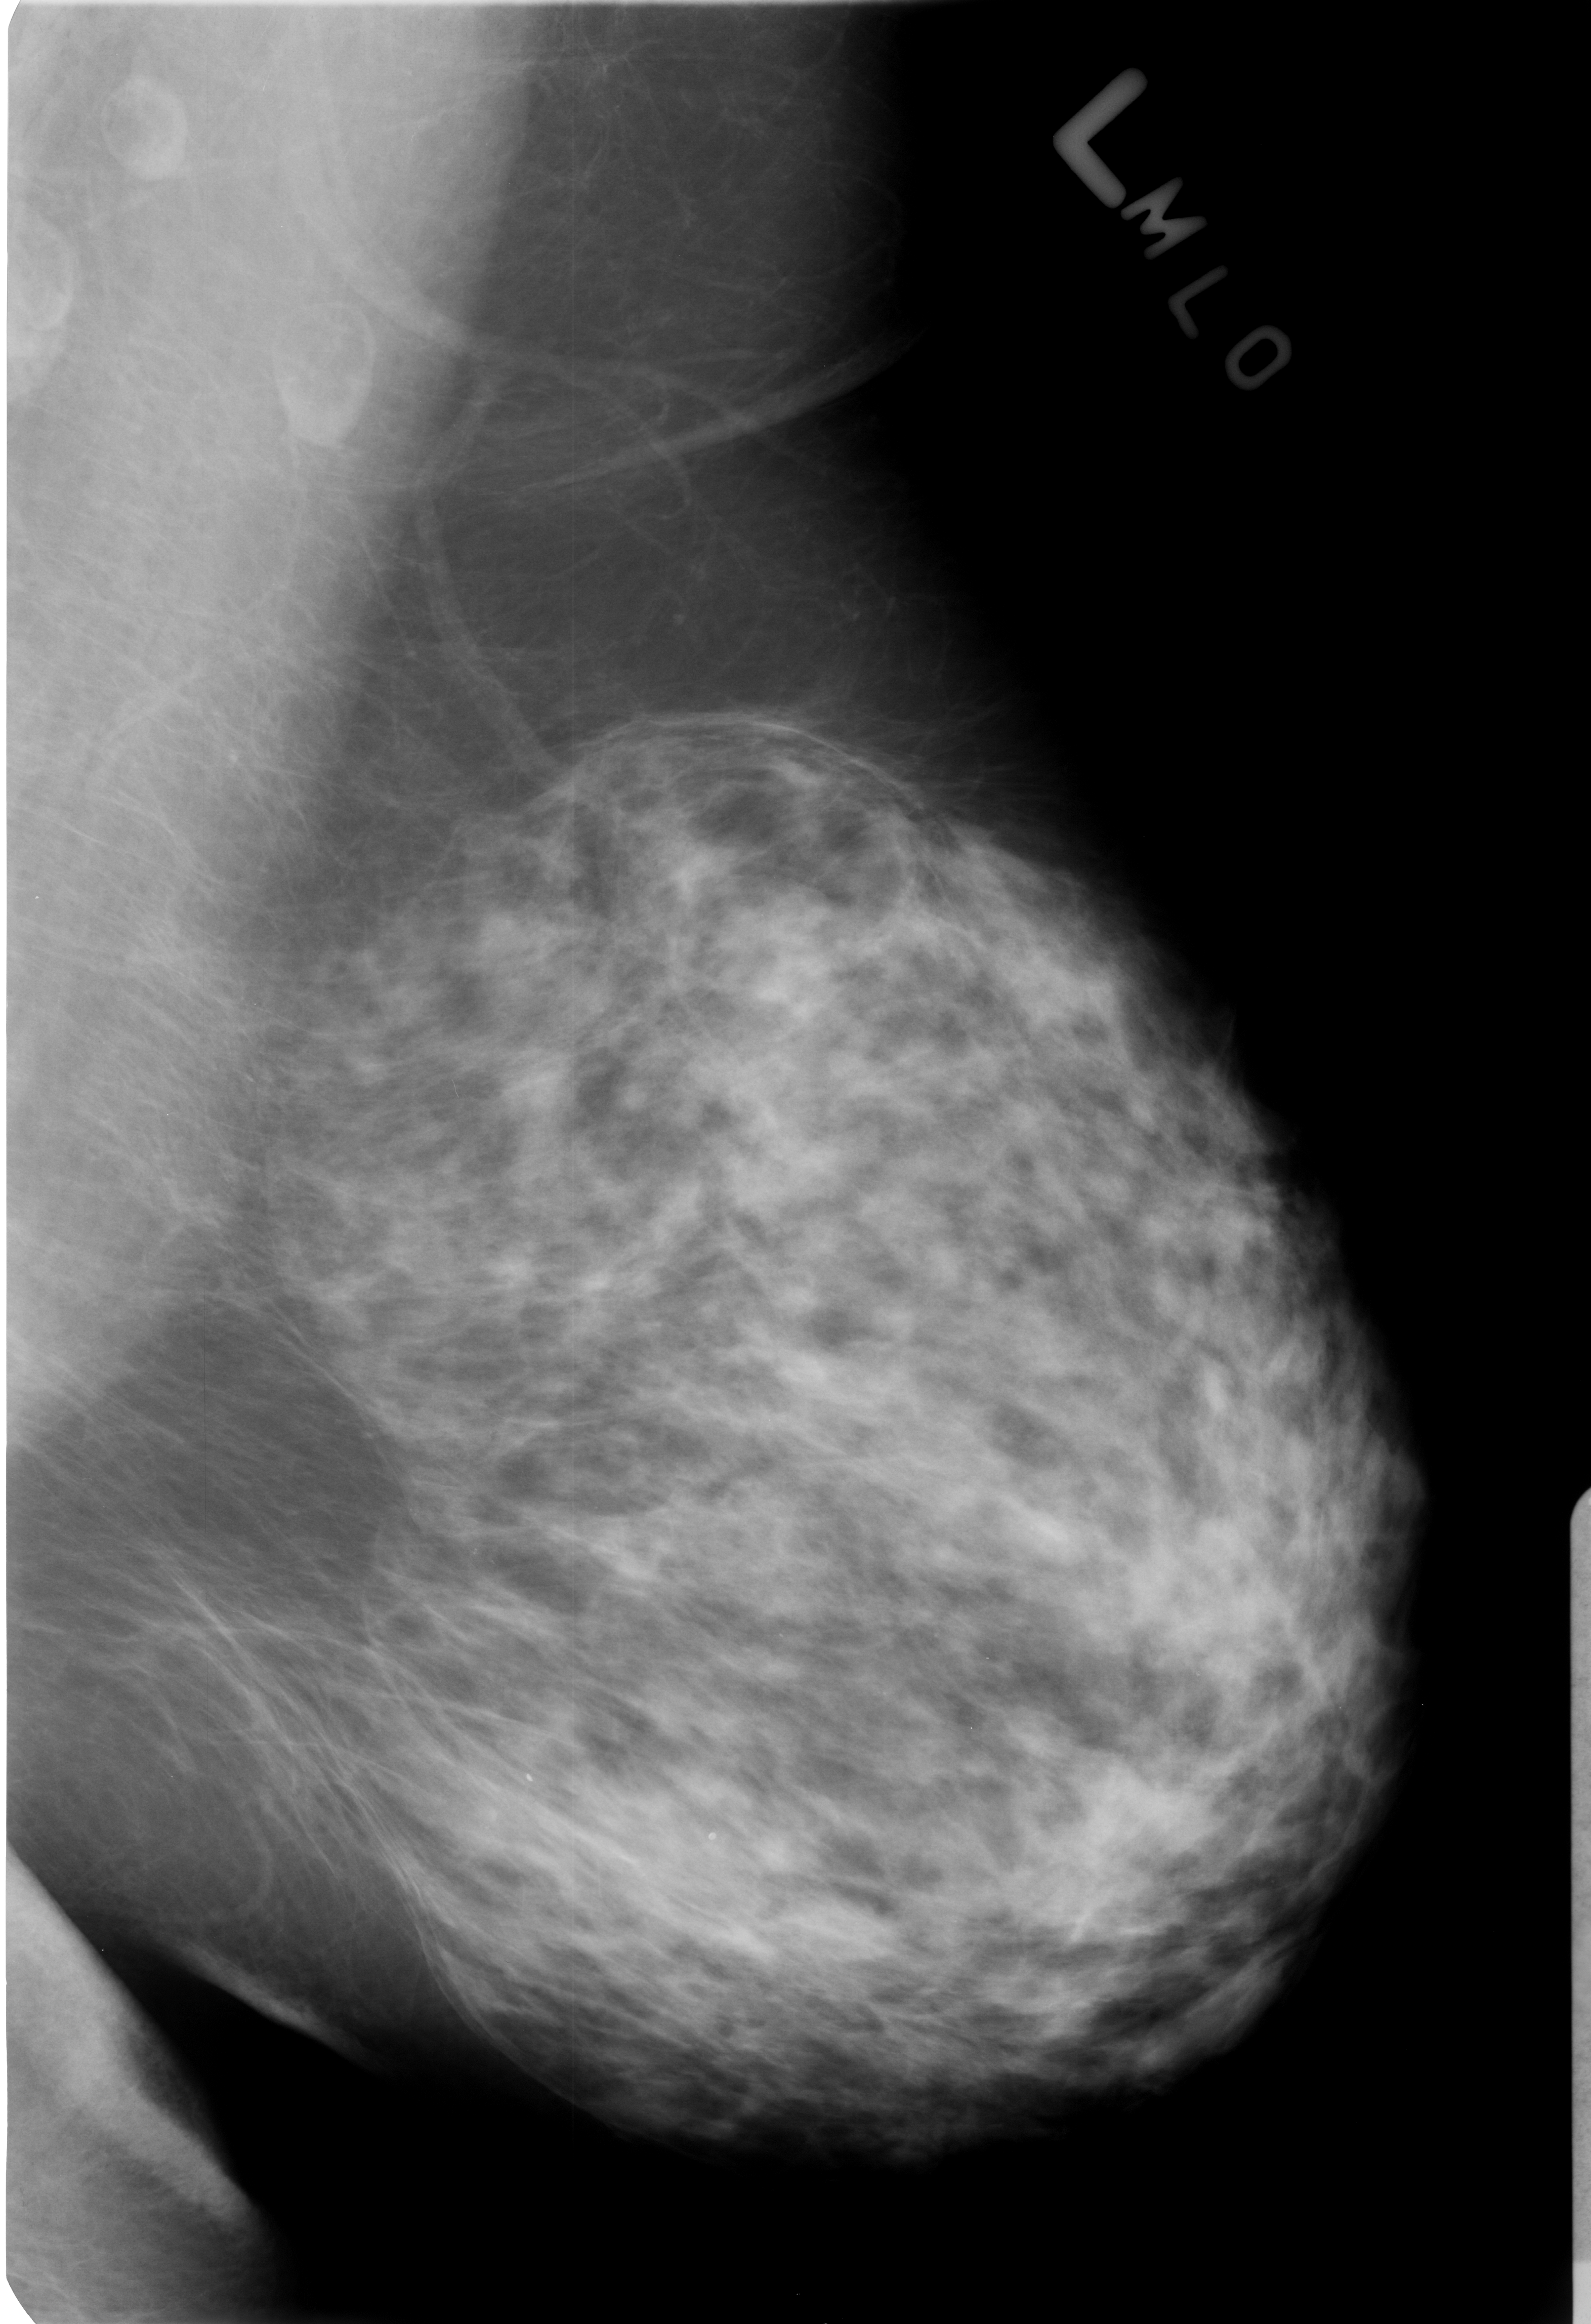
Mammogram (digitized film), left breast, mediolateral oblique (MLO) view, BI-RADS breast density category 3 (scale 1–4).
Abnormality record for this image: Finding 1 of 2: calcifications, morphology lucent center; BI-RADS assessment category 2; subtlety rating 3 on a 1 (subtle) to 5 (obvious) scale; benign; no additional work-up was recommended (benign without callback). Finding 2 of 2: calcifications, morphology lucent center; BI-RADS assessment category 2; subtlety rating 3 on a 1 (subtle) to 5 (obvious) scale; benign; no additional work-up was recommended (benign without callback).